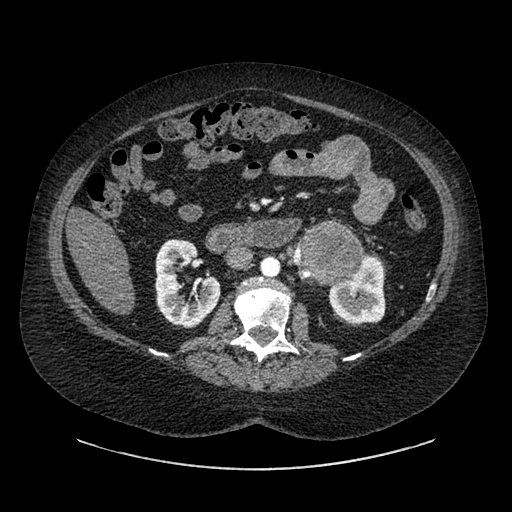
Contrast-enhanced abdominal CT, one axial slice; position 504 of 769 along the scan axis; reconstruction kernel SOFT; intravenous contrast given; soft-tissue window (W 400 / L 40 HU); 512 × 512 image matrix, field of view 460 × 460 mm. Female patient, age 61 years. Case-level facts recorded for this patient, not image findings: diagnosis: adrenocortical carcinoma; tumour side: left adrenal.
Structures marked on this image (semi-automatically segmented with operator editing):
- mass: box from (x=297, y=225) to (x=362, y=281) px